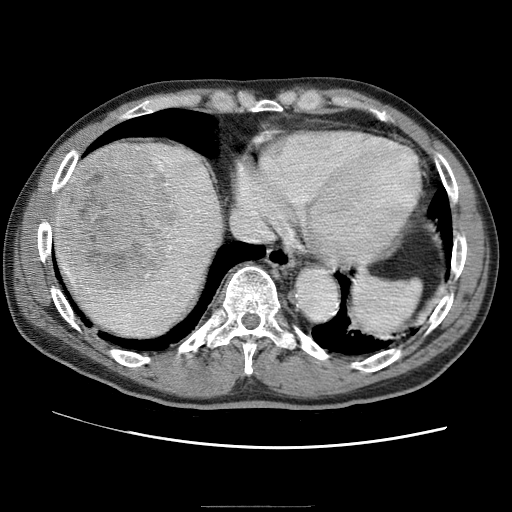
Contrast-enhanced abdominal CT (liver protocol), one axial slice; reconstruction kernel STANDARD; one of 2 acquisitions stored at this slice position; soft-tissue window (W 400 / L 40 HU); 512 × 512 image matrix, field of view 360 × 360 mm. From the clinical record (not read from this slice): diagnosis: hepatocellular carcinoma (patient treated with transarterial chemoembolisation; whether this scan precedes or follows treatment is not stated here); TNM stage (as recorded): Stage-II; Child-Pugh class: A; tumour differentiation: well differentiated; tumour size: 2 cm.
Annotated regions visible in this slice (semi-automatically segmented with operator editing):
- liver parenchyma outside the tumour (the mass and vessels are separate outlines, so this box may not span the whole liver): bounding box <52,140,226,340> (left, top, right, bottom; pixels)
- mass: <56,142,181,300>
- liver vessels: <133,167,180,295>